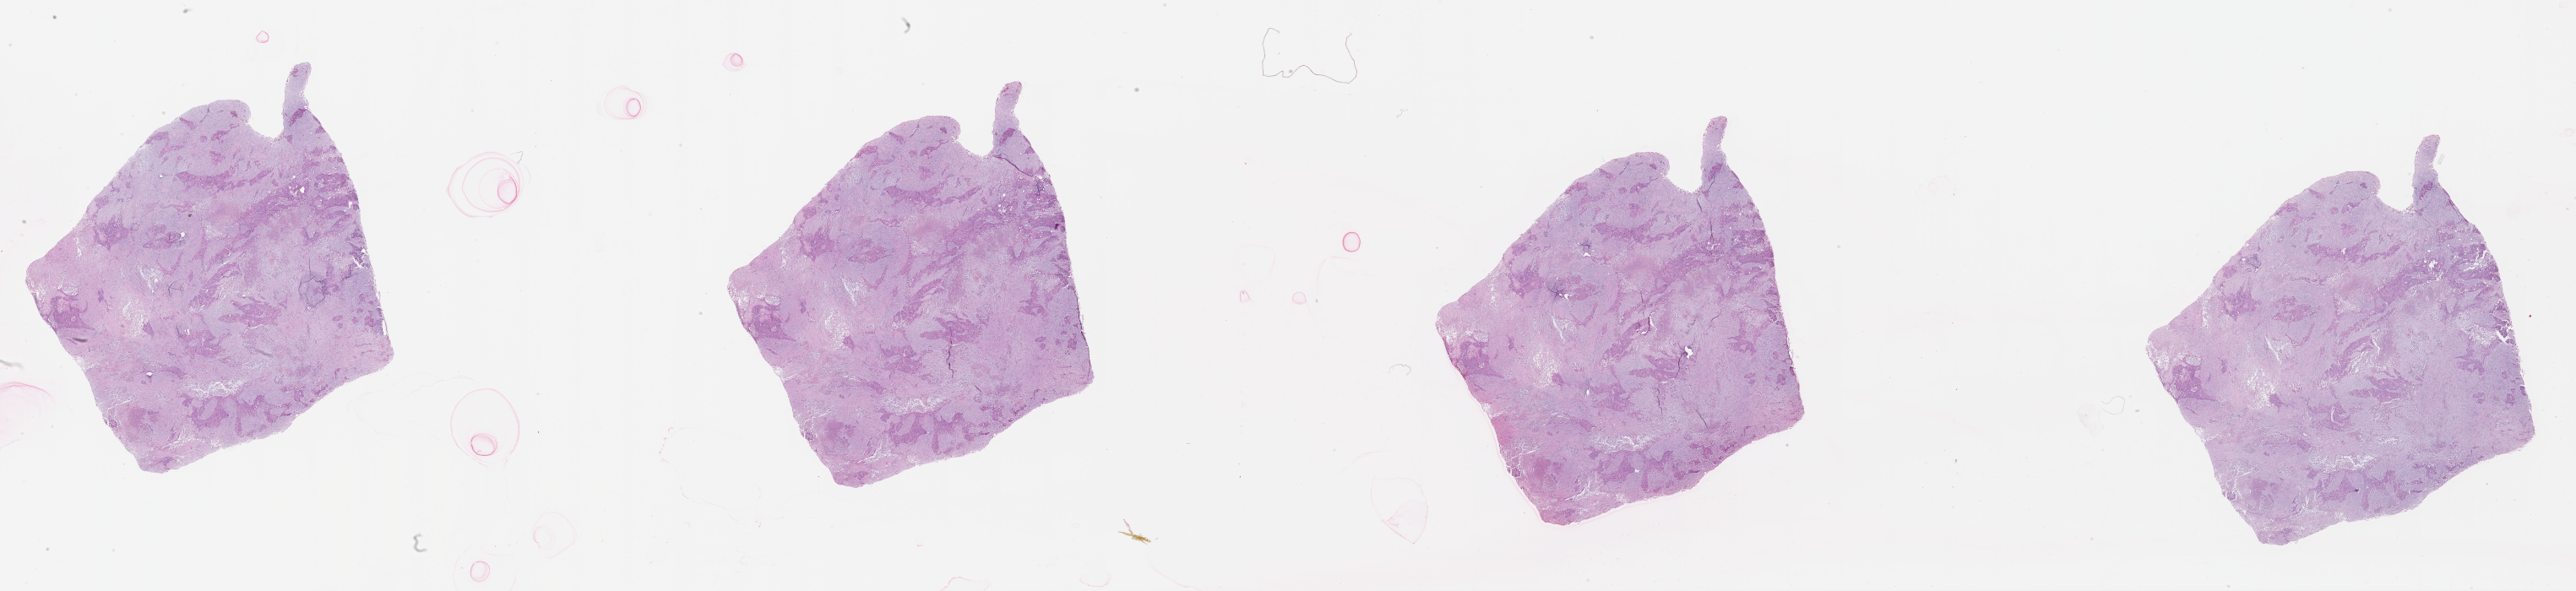
Whole-slide histology image, H&E, a low-resolution overview of the entire scanned area, about 49.1 x 11.3 mm (from a 20x scan), tumour tissue sample, lung. Male, 74 y/o.
Patient diagnosis (cohort enrolment): squamous cell carcinoma (lung).